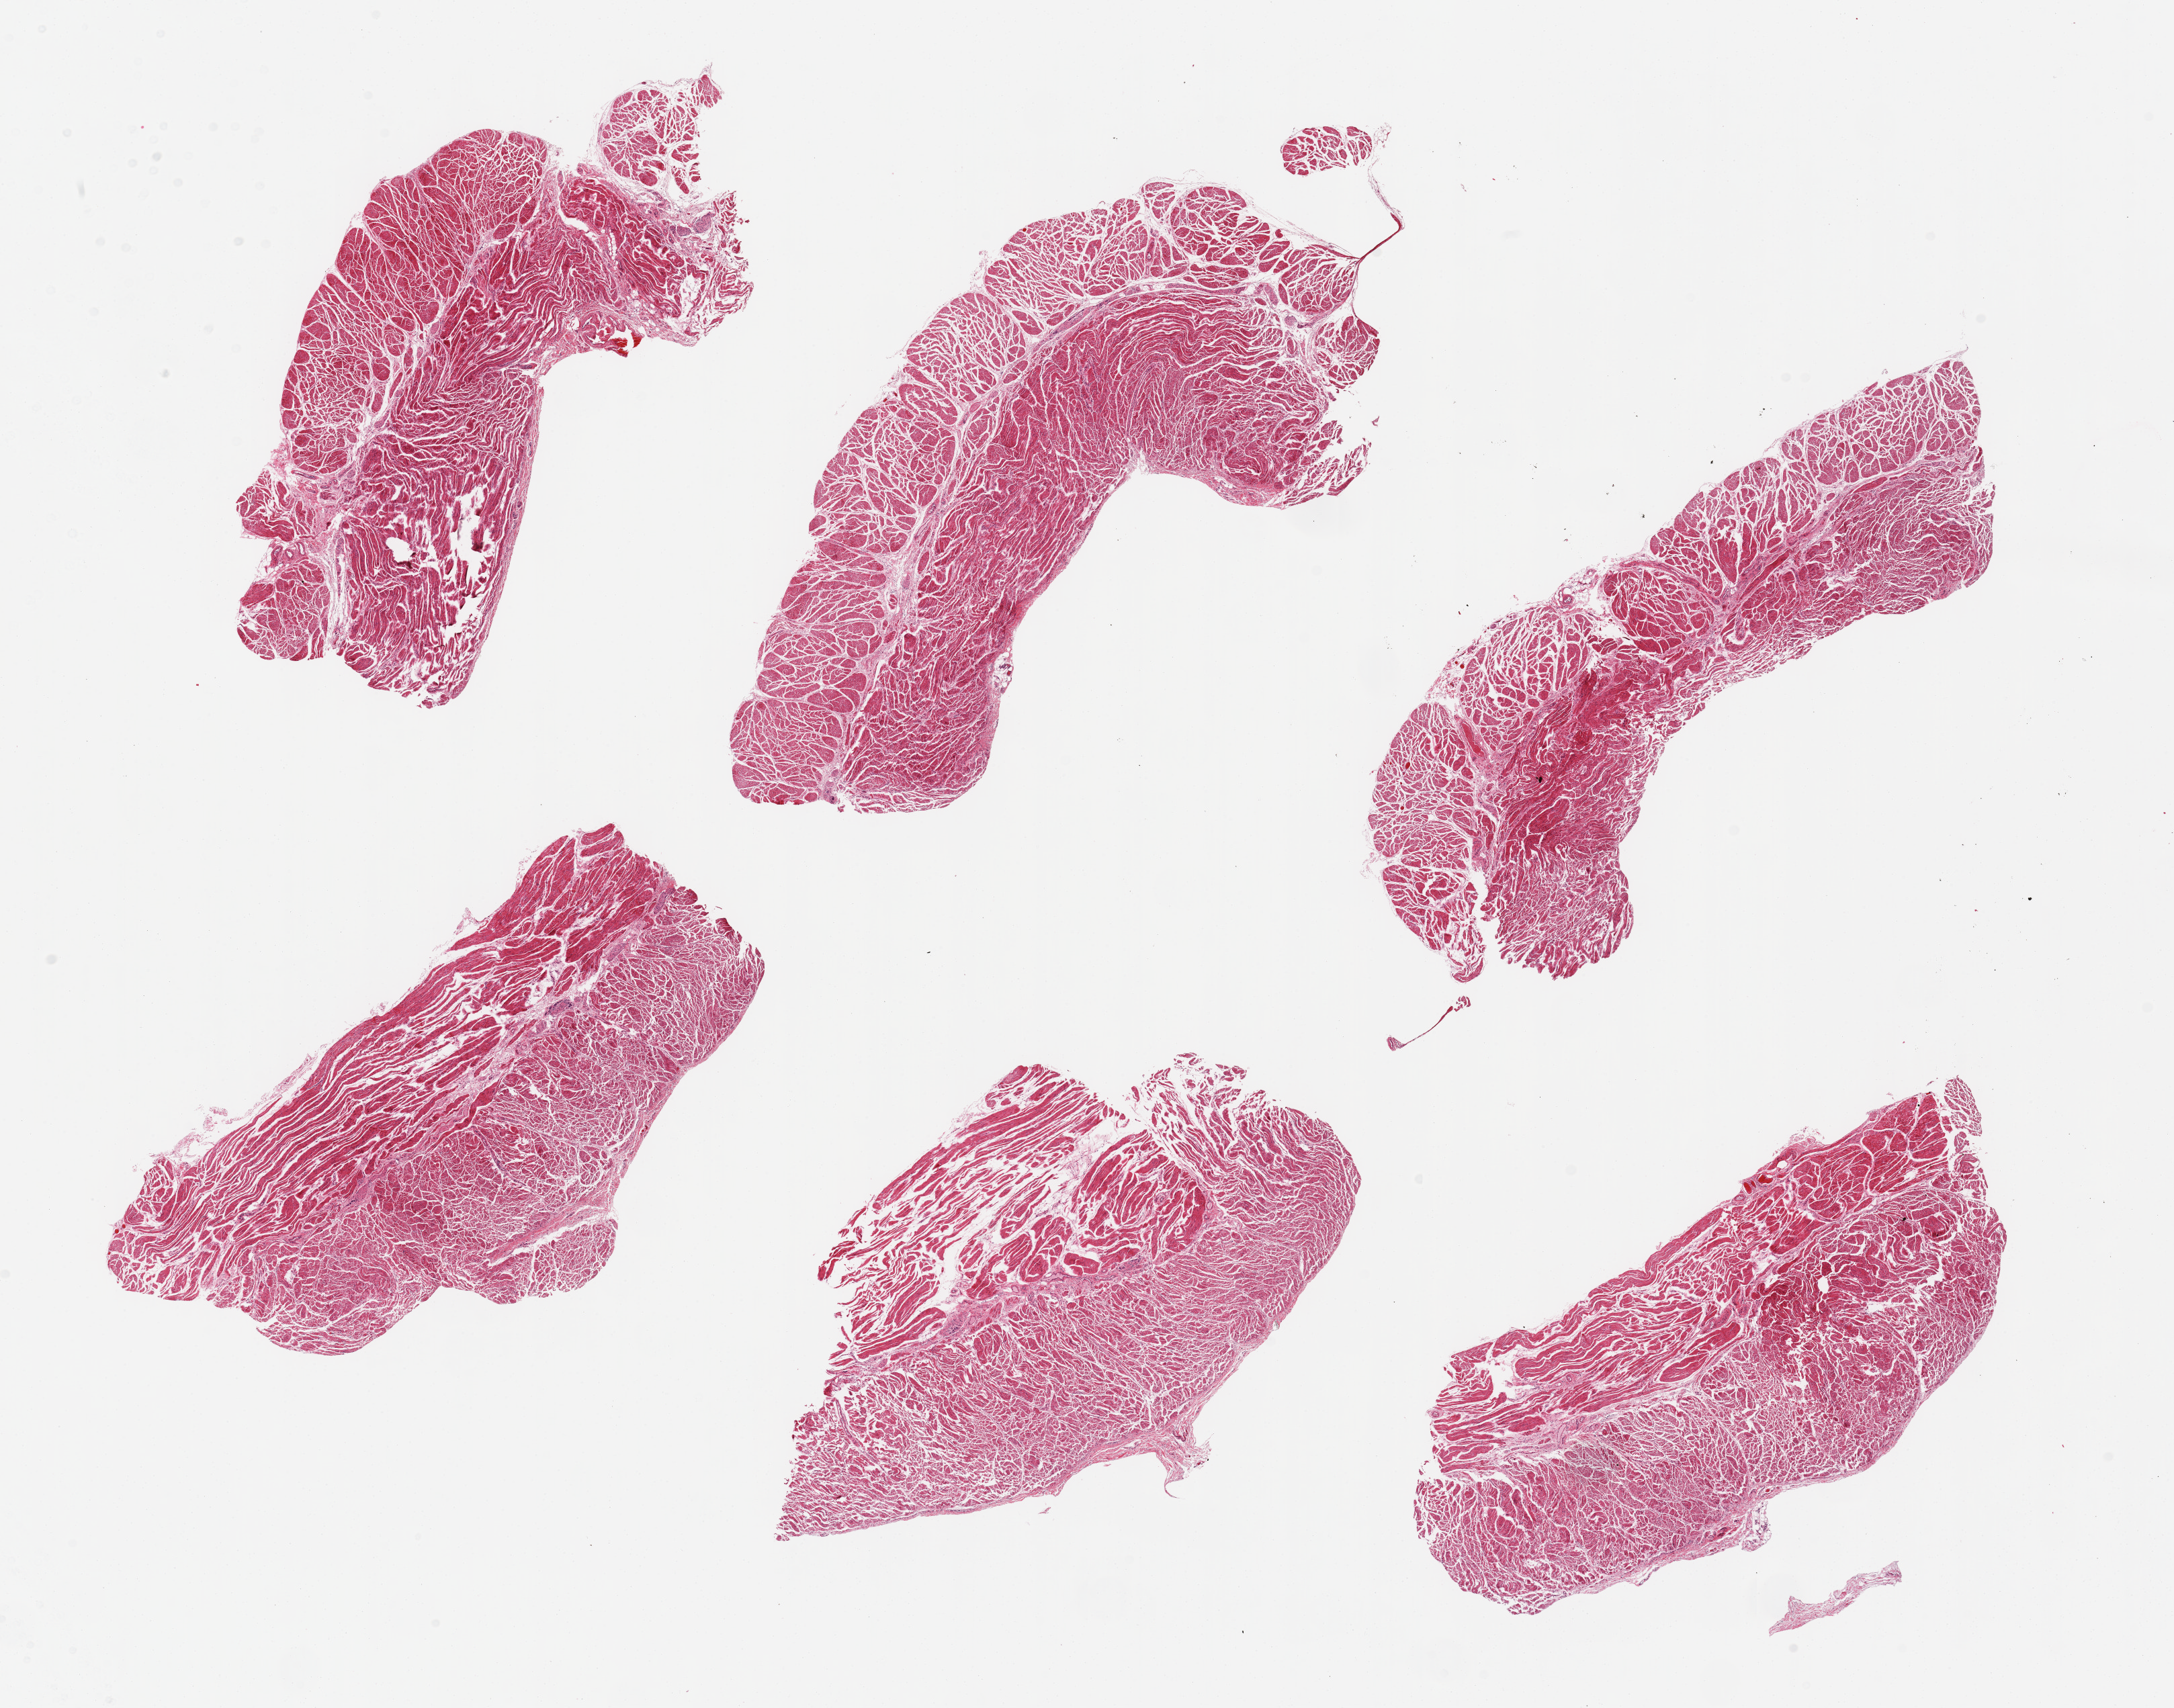
Whole-slide image, H&E stain, brightfield, shown as a low-resolution overview of the whole scanned area (about 25.6 x 20.1 mm); PAXgene-fixed paraffin-embedded (PFPE) section; section of gastroesophageal junction (target tissue); tissue donor sample. Donor: male.
Reviewer comment on this tissue sample: 6 pieces; well trimmed.